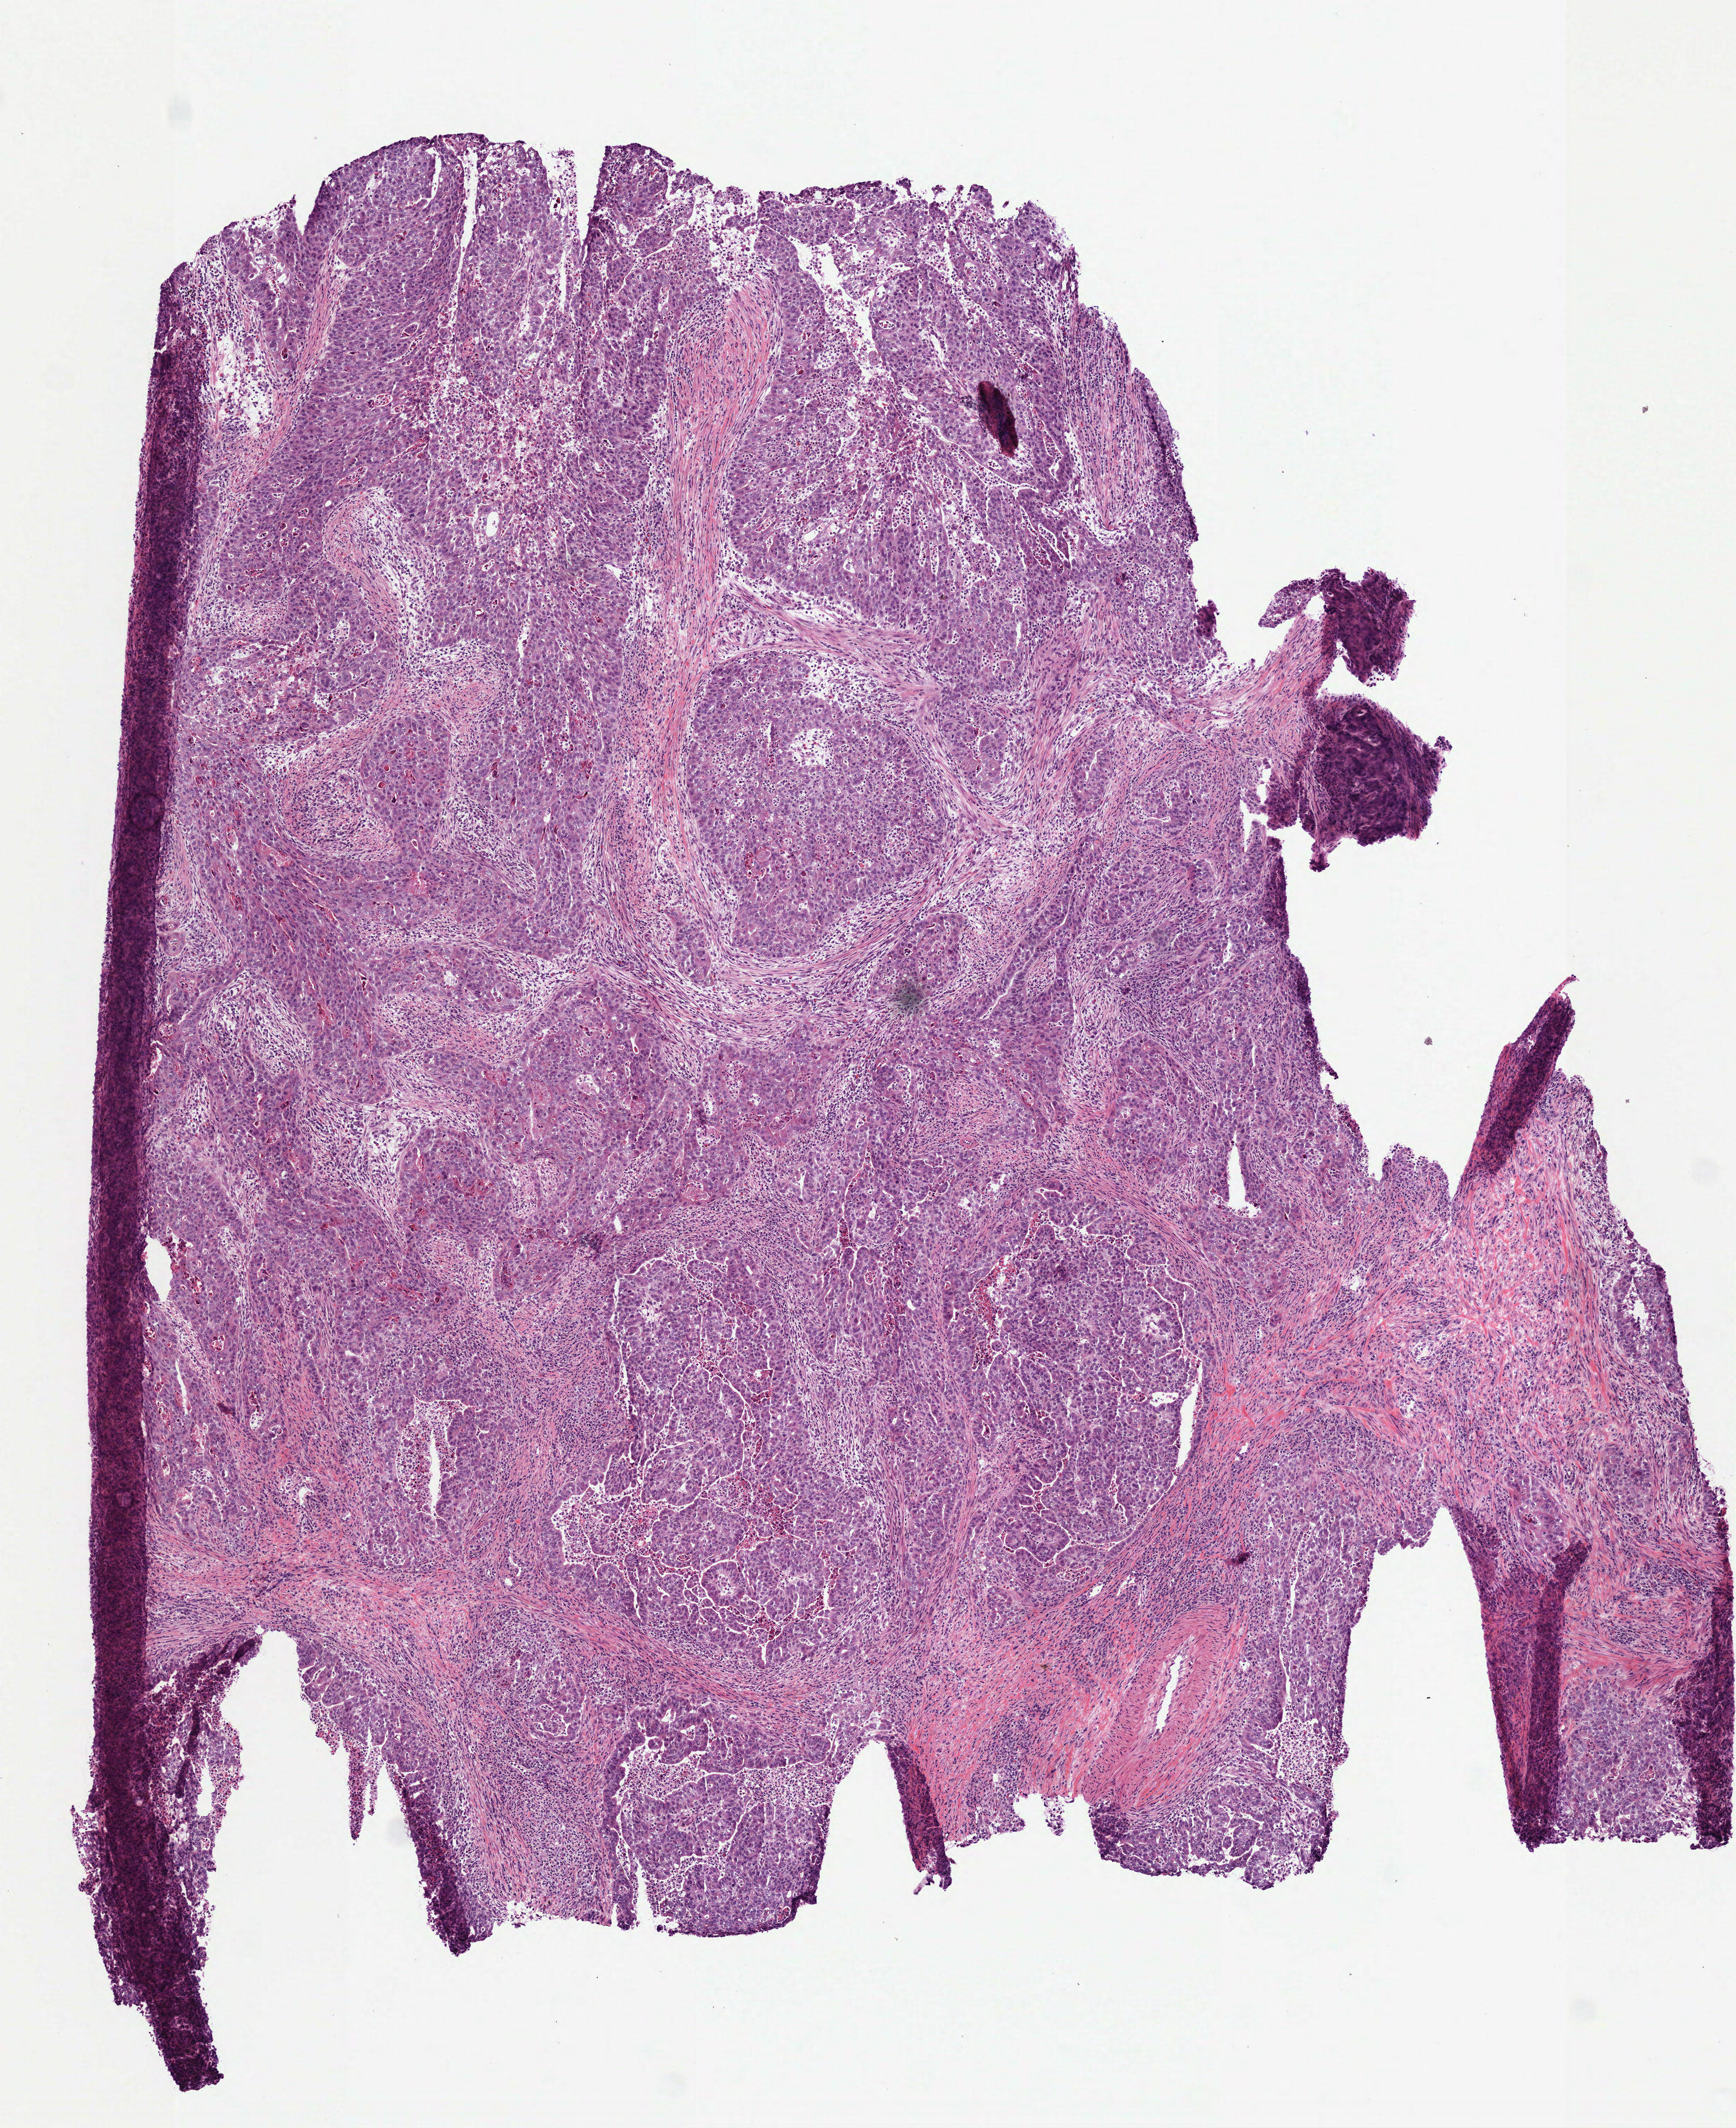
Whole-slide histology image, Hematoxylin and eosin (H&E) stained, shown as a low-resolution overview of the whole scanned area (about 5.0 x 6.2 mm); frozen section from the bottom of the tissue portion; sample: primary tumour, stomach. Male, age 57 years at initial diagnosis. Histologic grade: G3 (poorly differentiated). Slide review estimates, as recorded: tumour cells 86%, tumour nuclei 80%, normal cells 0%, stromal cells 5%, necrosis 9%. Inflammatory infiltration, as recorded: lymphocyte infiltration 9%, monocyte infiltration 0%, neutrophil infiltration 9%.
Histologic diagnosis: Tubular adenocarcinoma (fundus of stomach). AJCC pathologic stage: IIA (7th edition). Lymph nodes positive (case pathology): 0 of 20 examined.